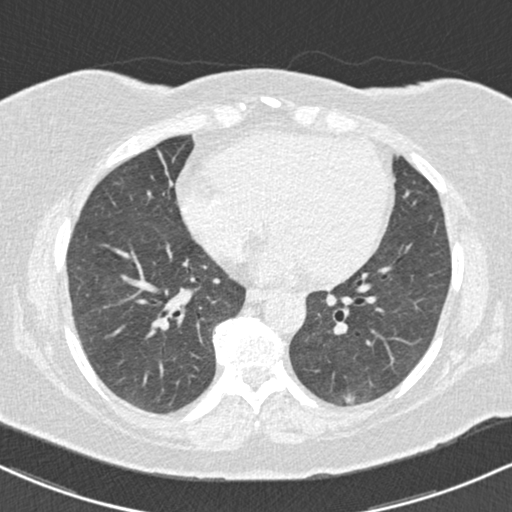
Low-dose screening chest CT, one axial slice. Position 65 of 147 along the scan axis. 120 kVp. Lung window (W 1500 / L -600 HU). 2 mm slice thickness. 512 × 512 image matrix, field of view 322 × 322 mm.
Structures marked on this image (expert manual segmentation):
- lesion 1 (tumor, lower lobe of left lung): bounding box (x1, y1, x2, y2) in pixels: (344, 394, 355, 404)